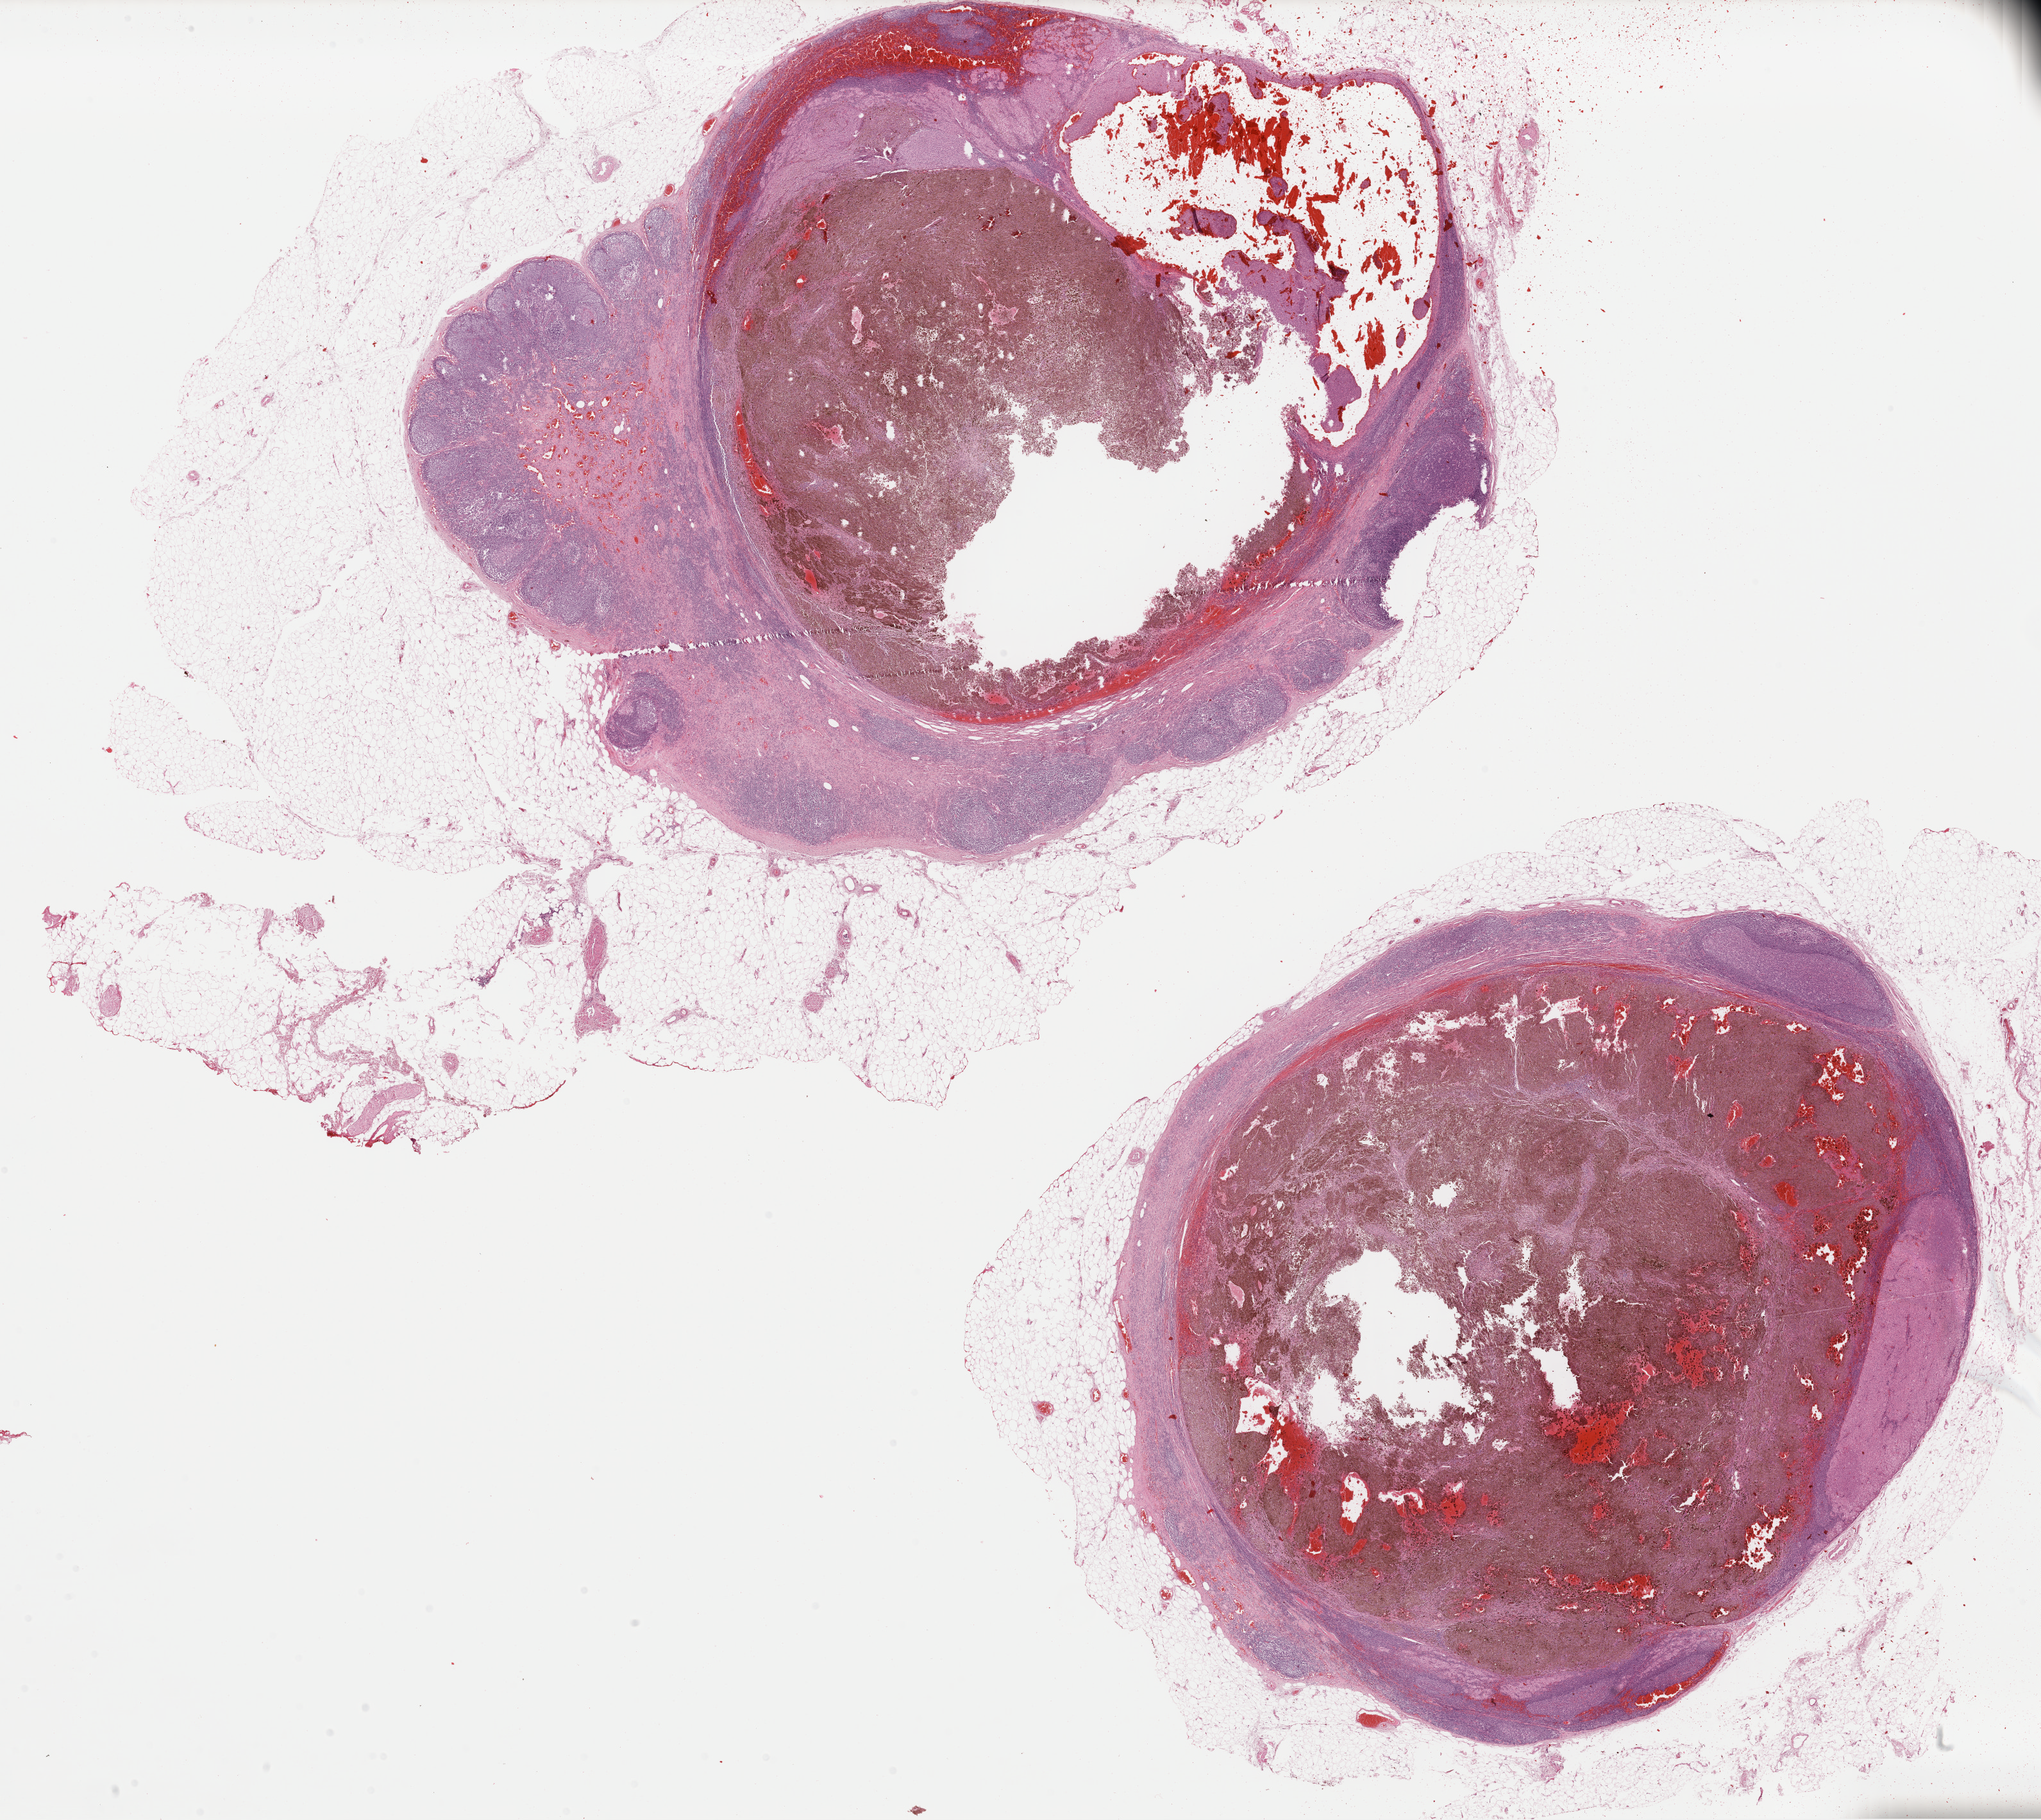
Whole-slide histology image, Hematoxylin and eosin (H&E) stained — whole scanned area (about 25.1 x 22.4 mm) shown as a low-resolution overview. Formalin-fixed paraffin-embedded (FFPE) diagnostic section. Metastatic tumour sample, sampled site not recorded. Patient: female, age at initial diagnosis 80 years.
* this section: metastatic tumour tissue
* patient diagnosis: Malignant melanoma, NOS